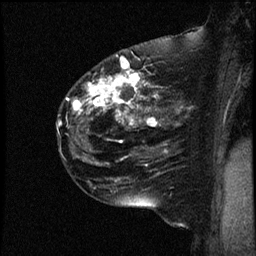
Breast MRI (dynamic contrast-enhanced), one sagittal slice. Slice 33 of 44 in the series (ordered by position). Dynamic contrast-enhanced study with each time point stored as its own series, time point 2 of 4 at this slice position (early post-contrast, ordered by acquisition time). 1.5 T. TE 4.2 ms, TR 17.7 ms. 2 mm slice thickness. 256 × 256 image matrix, field of view 200 × 200 mm. Female patient, age 52 years. Case-level facts recorded for this patient, not image findings: setting: breast cancer imaged before/during neoadjuvant chemotherapy; receptor status: HR-positive, HER2-negative.
Structures marked on this image (semi-automatic segmentation, software-assisted and operator-edited):
- analysis volume of interest (the breast-tissue region the enhancement analysis was run in; not a lesion): bounding box [x1, y1, x2, y2] px = [56, 48, 163, 147]
- tumour enhancement mask (voxels above the 100 % enhancement threshold inside the analysis volume of interest): [57, 54, 158, 136]